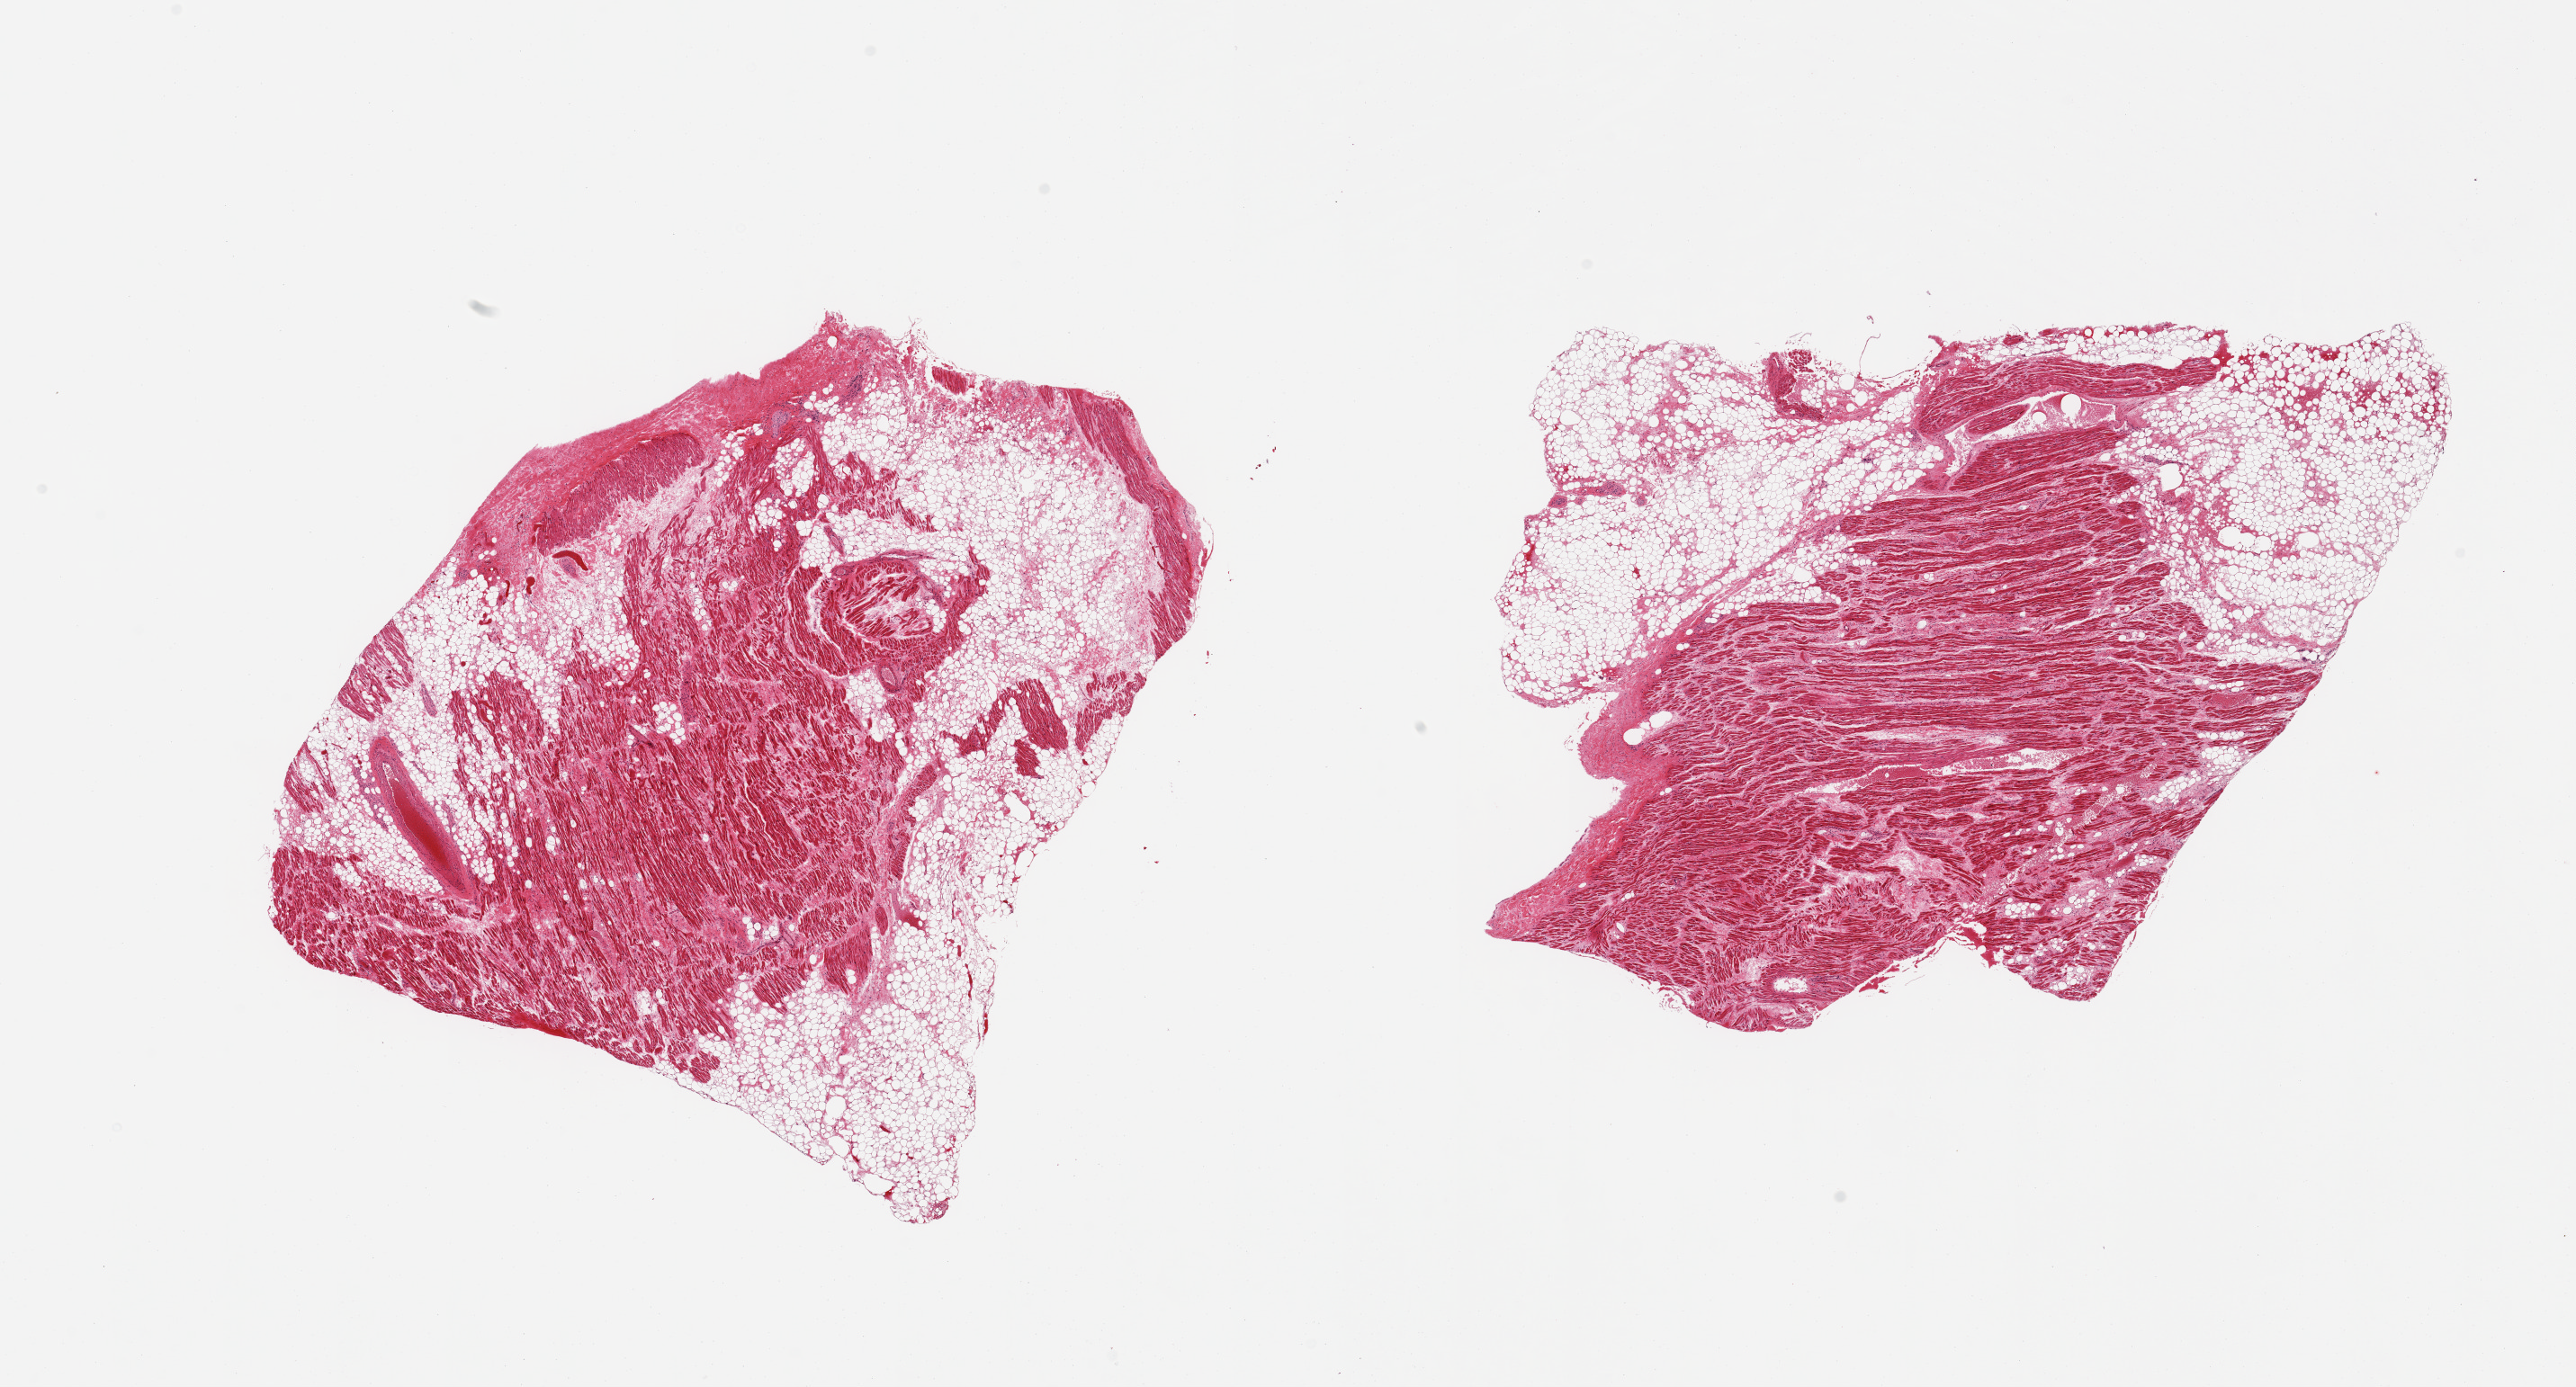
Whole-slide image, hematoxylin and eosin (H&E) stain, low-resolution overview of the scanned area, about 22.6 x 12.2 mm (slide scanned at 20x), PAXgene-fixed paraffin-embedded (PFPE) section, sampled site (target tissue): auricular appendage, donor tissue sample. Donor sex: female.
• pathologist's review note for this sample: 2 pieces; 50% adipose